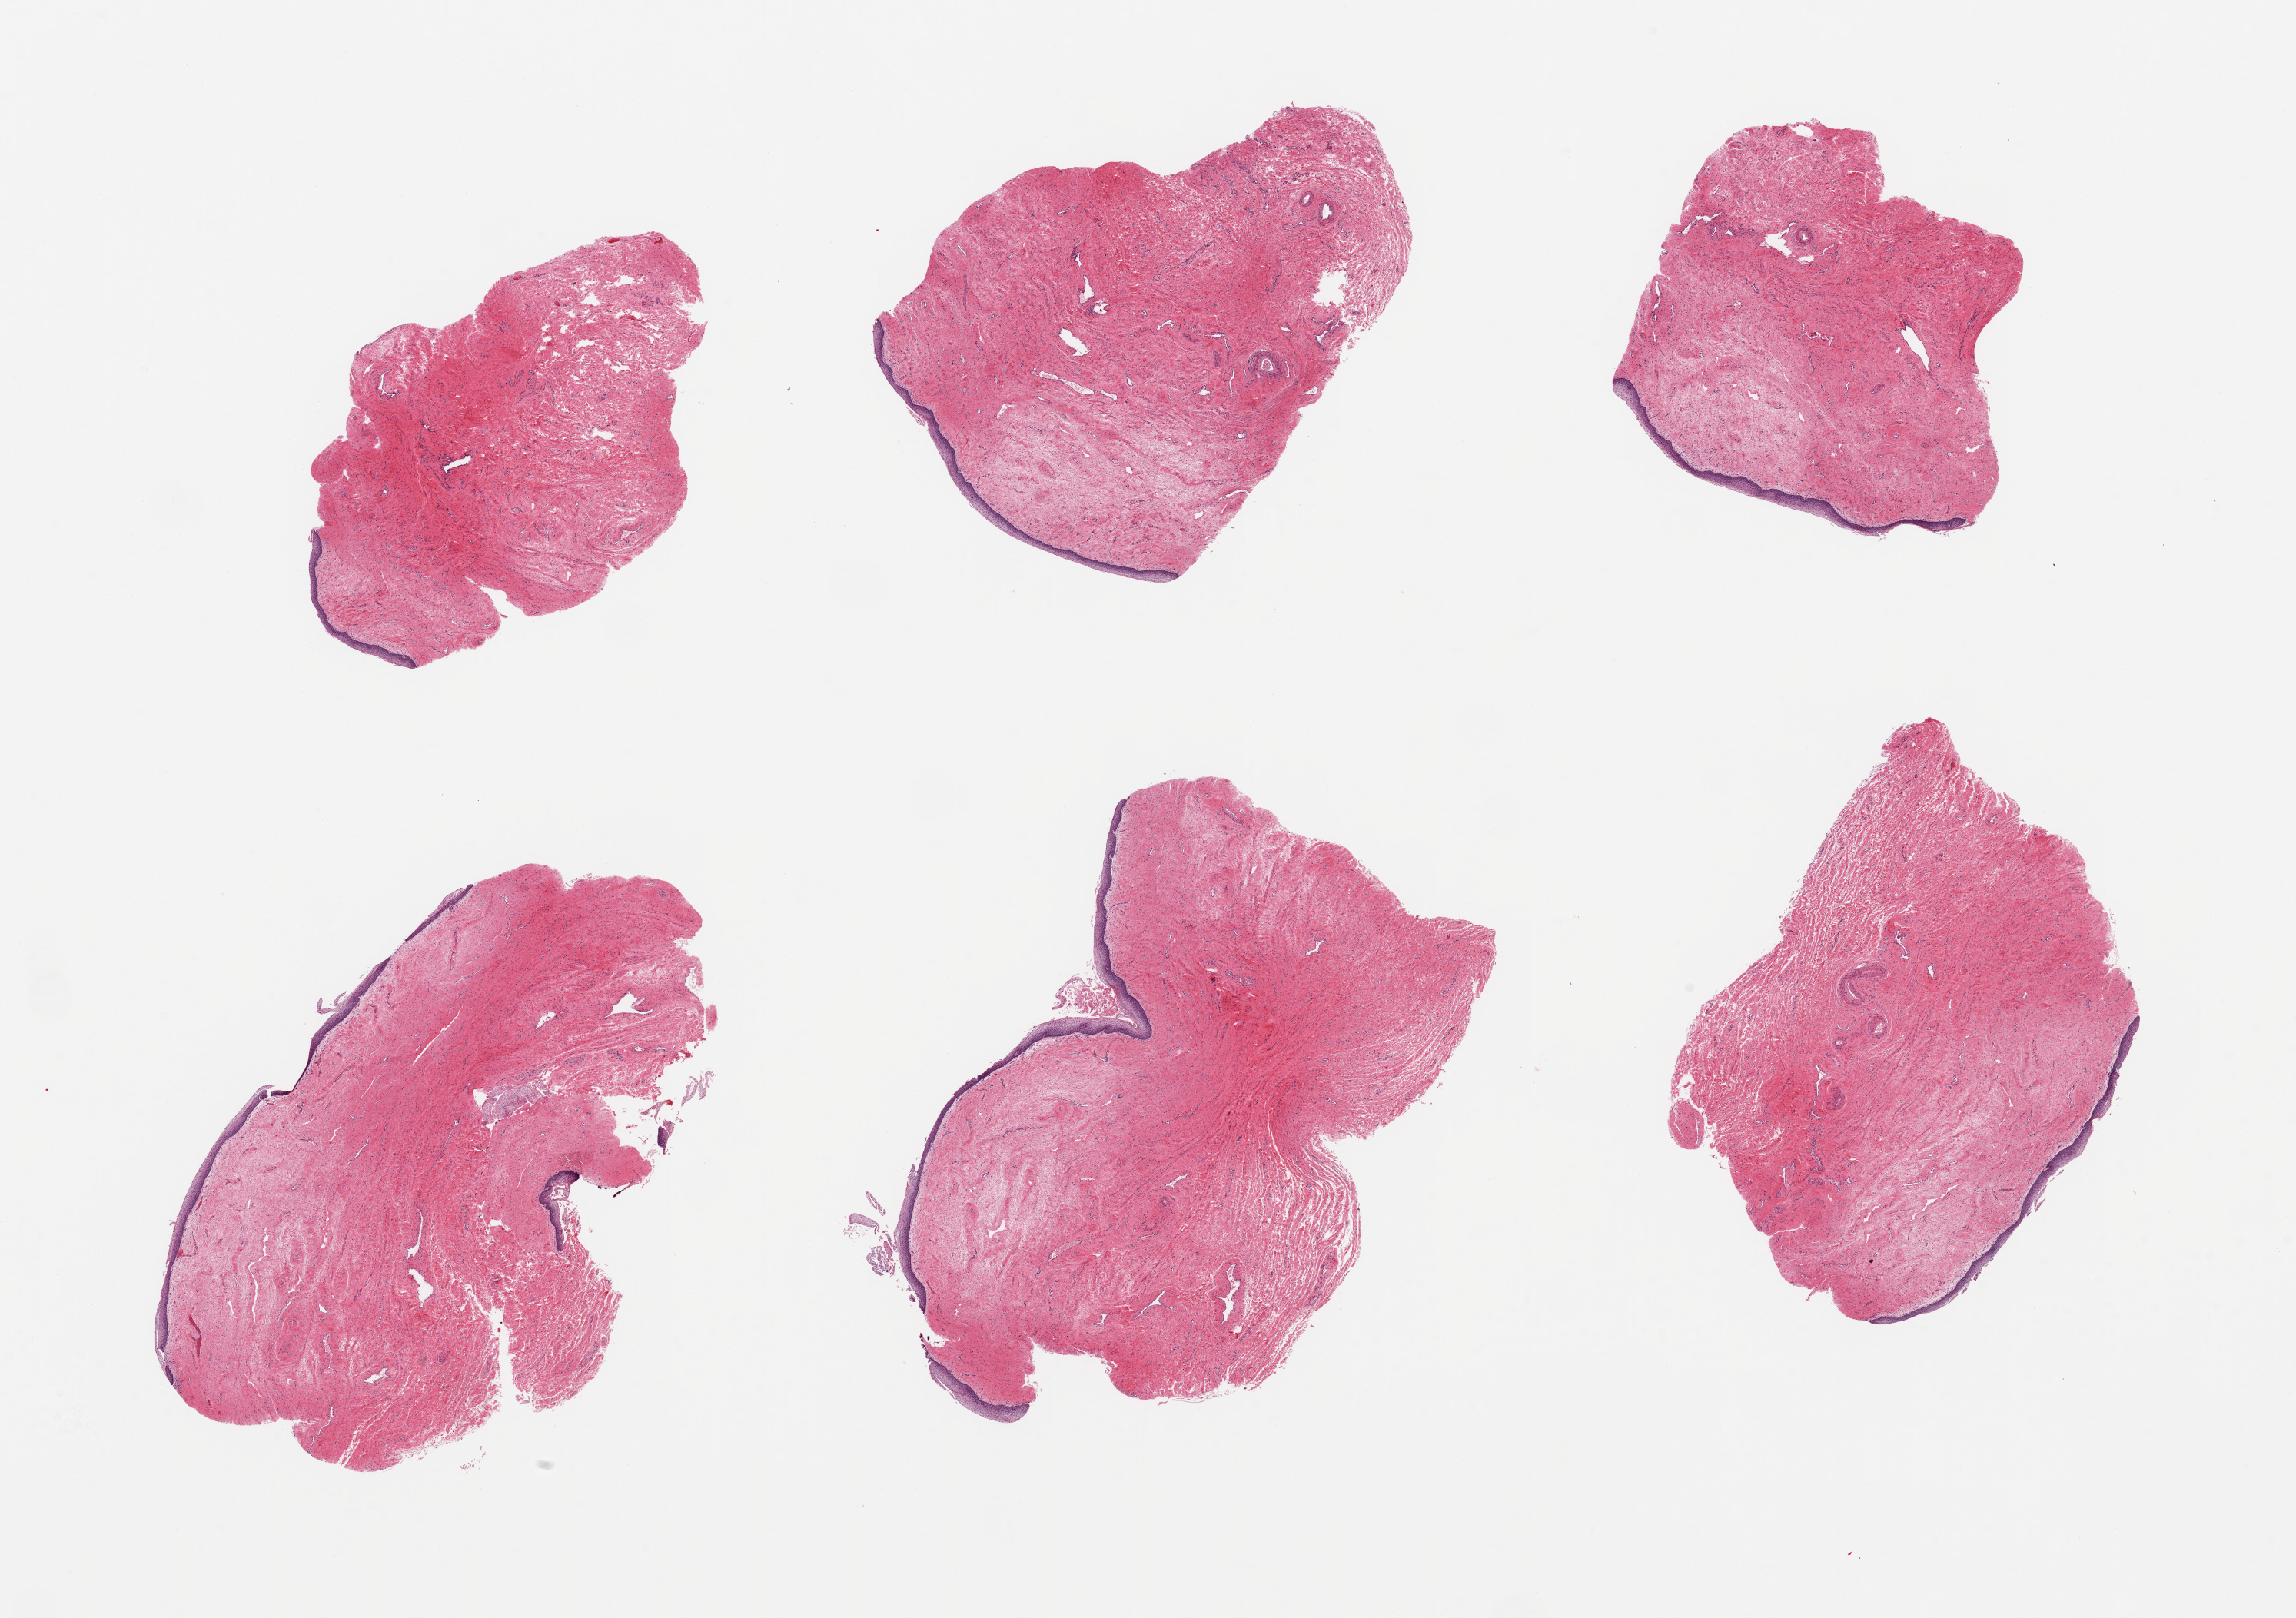
Whole-slide image, hematoxylin and eosin (H&E) stain — shown as a low-resolution overview of the whole scanned area (about 23.6 x 16.6 mm, from a 20x scan), PAXgene-fixed paraffin-embedded (PFPE) section, section of vagina (target tissue), donor tissue sample. Donor sex: female.
• reviewer comment on this tissue sample: 6 pieces; epithelium preserved